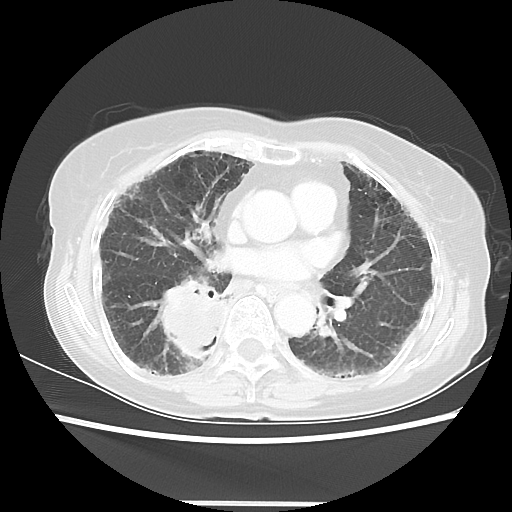
Chest CT, one axial slice. Slice 27 of 52 in the series (ordered by position). Reconstruction kernel LUNG. 120 kVp. Lung window (W 1500 / L -600 HU). 5 mm slice thickness. 512 × 512 image matrix. Female patient, age 71 years. Case-level facts recorded for this patient, not image findings: clinical TNM (as recorded): T3 N0 M0.
Annotated regions visible in this slice (bounding box drawn by a radiologist):
- lung tumour (recorded histology: squamous cell carcinoma): bounding box (x1, y1, x2, y2) in pixels: (149, 275, 222, 362)